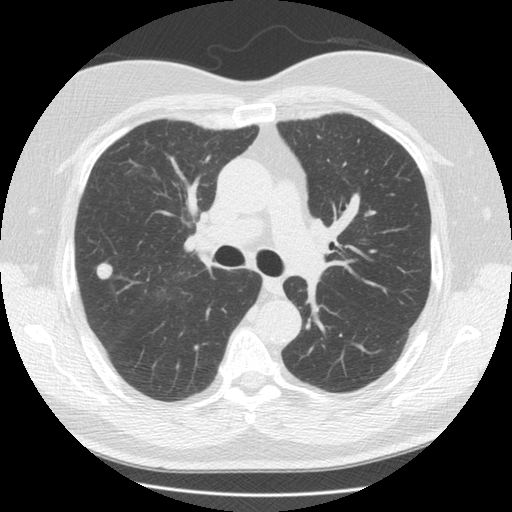
Chest CT (low-dose screening protocol), one axial image. Third screening round (two years after baseline). Lung window (W 1500 / L -600 HU). Standard (soft-tissue) reconstruction kernel (STANDARD). Male participant, aged 65 years at enrolment. Former smoker at enrolment.
Expert reader's lesion annotation, bounding box [x1, y1, x2, y2] px = [90, 258, 117, 286]. Screening reader's record for this exam (one nodule recorded; not confirmed to be the boxed lesion): non-calcified nodule or mass ≥4 mm, right upper lobe, 12 × 12 mm, smooth margins, soft tissue attenuation, pre-existing on the prior screen: yes; interval growth: yes. Official screen result: positive, other.